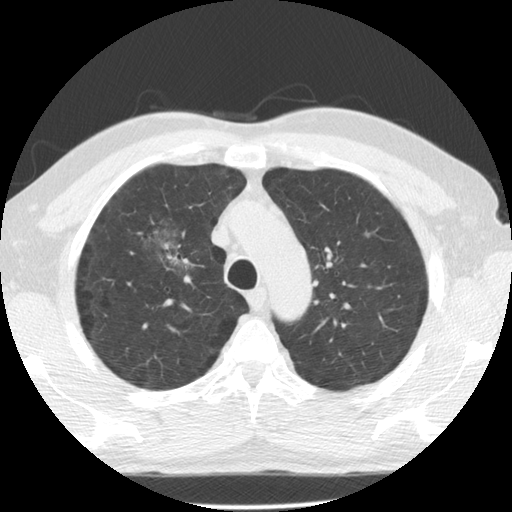
Chest CT (low-dose screening protocol), one axial image. Second screening round (one year after baseline). Lung window (W 1500 / L -600 HU). 2.5 mm slice thickness. Slice 98 of 135 in the series. Male participant, aged 60 years at enrolment. Former smoker at enrolment.
Expert reader's lesion annotation, box from (x=133, y=216) to (x=196, y=277) px. The exam's reader record, not a measurement of the box and not confirmed to be the same lesion: non-calcified nodule or mass ≥4 mm, right upper lobe, poorly defined margins, mixed attenuation, pre-existing on the prior screen: yes; interval growth: yes.